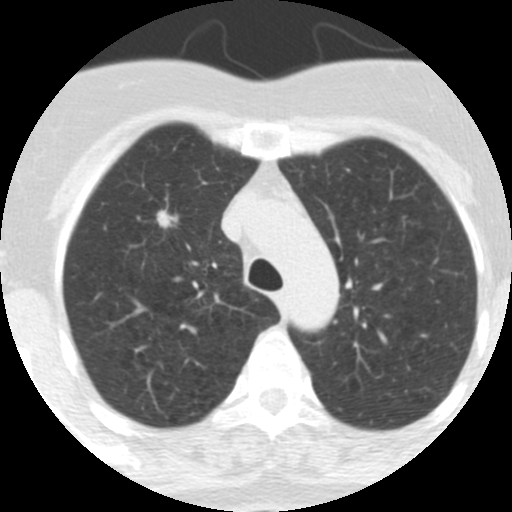
Axial slice from a low-dose chest CT screening exam; first (baseline) screen; lung window (W 1500 / L -600 HU); standard (soft-tissue) reconstruction kernel (STANDARD); slice 75 of 313 in the series; 512 × 512 image matrix. Female participant, aged 62 years at enrolment. Current smoker at enrolment.
- Expert reader's lesion annotation, bounding box [x1, y1, x2, y2] px = [116, 160, 182, 232].
- Screening reader's record for this exam (one nodule recorded; not confirmed to be the boxed lesion): non-calcified nodule or mass ≥4 mm, right upper lobe, 9 × 7 mm, spiculated (stellate) margins, soft tissue attenuation.
- Official screen result: positive, change unspecified: nodule(s) >= 4 mm or enlarging nodule(s), mass(es), or other non-specific abnormalities suspicious for lung cancer.
- Later outcome: lung cancer diagnosed 126 days after this screen — adenocarcinoma, NOS, right upper lobe, moderately differentiated (G2), stage IA (AJCC 6th edition), 18 mm at pathology.